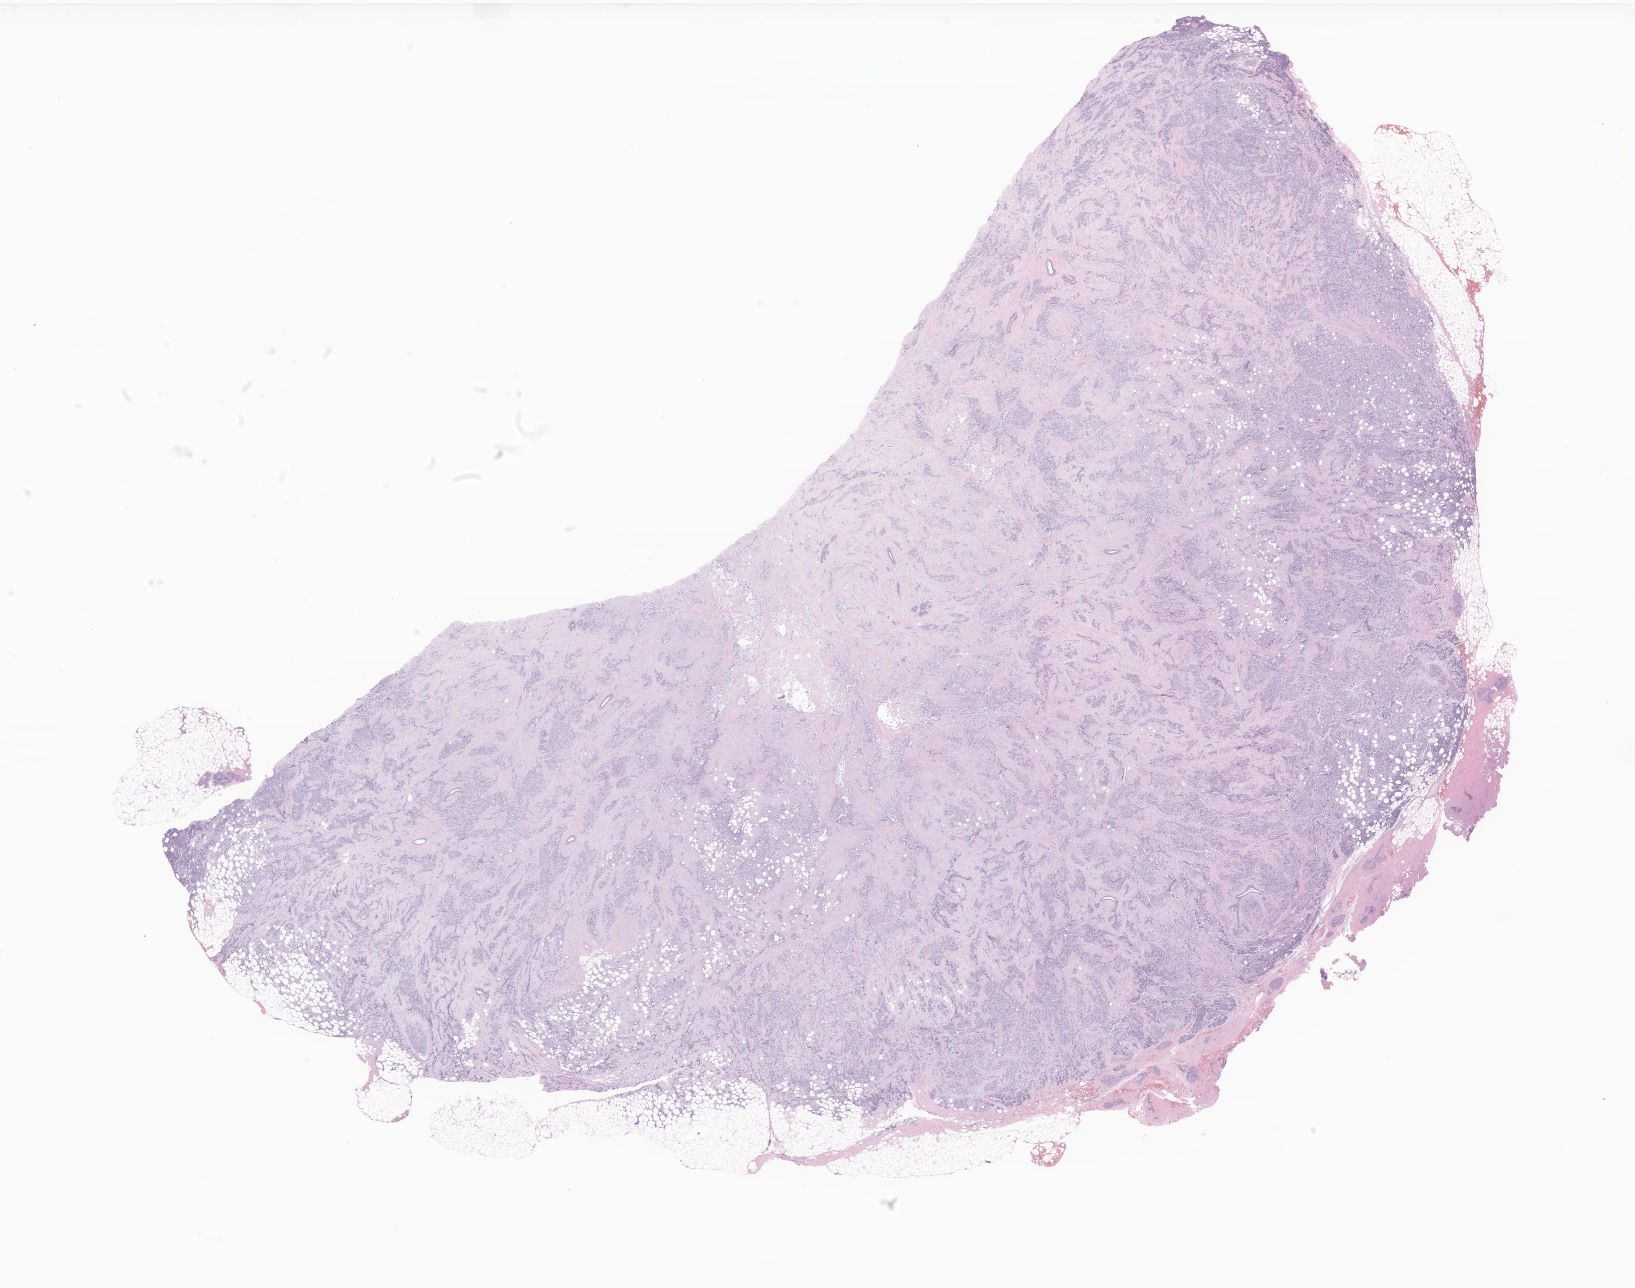
H&E whole-slide image of tumor tissue from the soft tissue of pelvis — low-resolution overview of the scanned area, about 27.6 x 21.7 mm; formalin-fixed, paraffin-embedded (FFPE) tissue. Patient: female, age 202 months.
* diagnosis (ICD-O-3 morphology term): Rhabdomyosarcoma, NOS